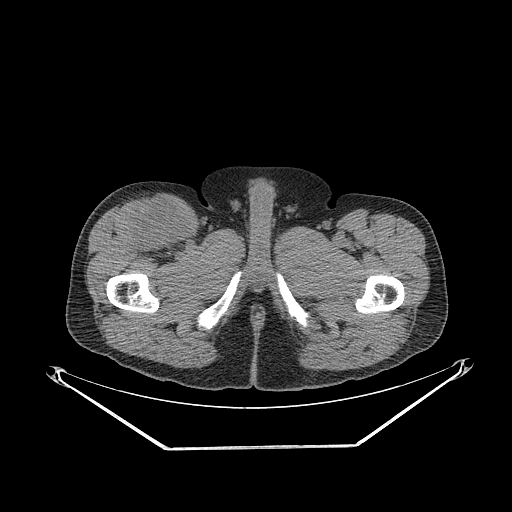
CT of an extremity soft-tissue mass (from a PET/CT study), one axial slice. Position 302 of 311 along the scan axis. 140 kVp. Soft-tissue window (W 400 / L 40 HU). 3.75 mm slice thickness. 512 × 512 image matrix, field of view 500 × 500 mm. Male patient. From the clinical record (not read from this slice): histological type: pleiomorphic leiomyosarcoma; grade: intermediate; site of the primary tumour: right thigh.
Outlined on this slice (expert contour drawn on MRI and transferred to this co-registered scan by the dataset authors):
- gross tumour volume including surrounding oedema: box from (x=130, y=198) to (x=191, y=252) px
- gross tumour volume (mass): (x=135, y=206)–(x=190, y=250)